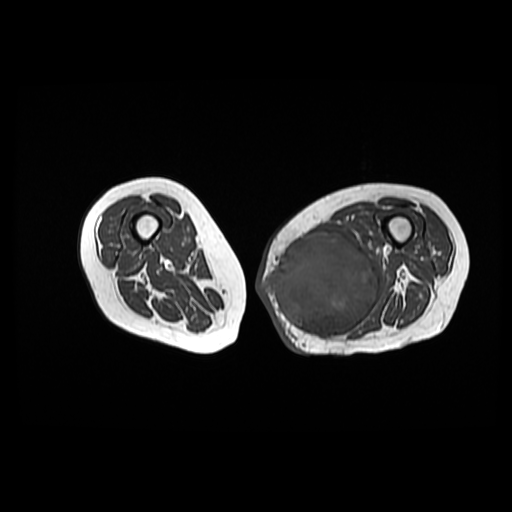
MRI of an extremity soft-tissue mass, one axial slice; position 30 of 42 along the scan axis; 512 × 512 image matrix, field of view 420 × 420 mm. Female patient. From the clinical record (not read from this slice): histological type: pleomorphic leiomyosarcoma; grade: high; site of the primary tumour: left thigh.
Outlined on this slice (expert manual segmentation):
- gross tumour volume including surrounding oedema: bounding box <263,230,380,338> (left, top, right, bottom; pixels)
- gross tumour volume (mass): <263,230,380,338>